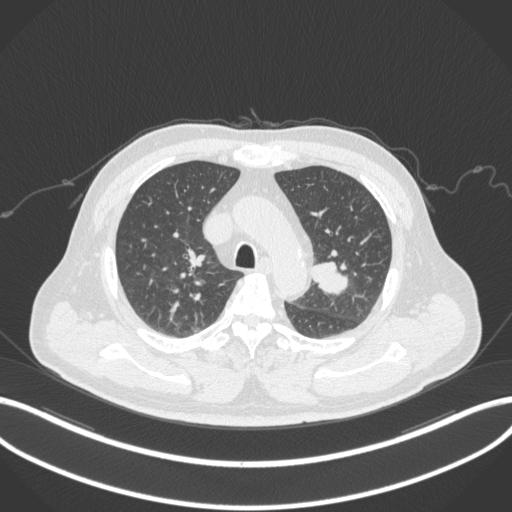
Chest CT, one axial slice; position 219 of 286 along the scan axis; reconstruction kernel B31f; 120 kVp; lung window (W 1500 / L -600 HU); 1 mm slice thickness; 512 × 512 image matrix, field of view 400 × 400 mm. Patient: male, 67 years. From the clinical record (not read from this slice): clinical TNM (as recorded): T2a N1 M0; histopathological grade: G3.
Annotated regions visible in this slice (rectangle marked by the reading radiologist):
- lung tumour (recorded histology: adenocarcinoma): bounding box (x1, y1, x2, y2) in pixels: (309, 257, 354, 299)